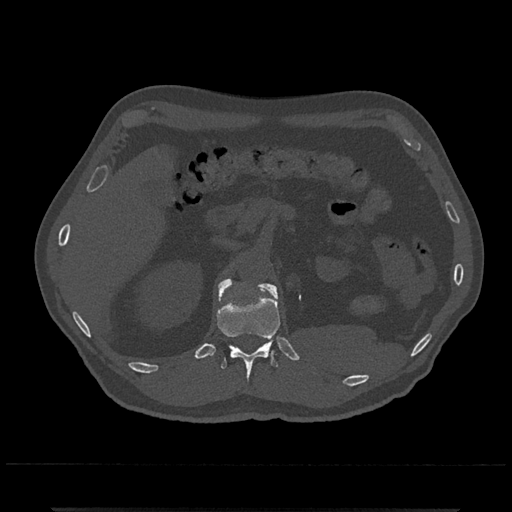
CT including the spine, one axial slice. Slice 418 of 797 in the series (ordered by position). Bone window (W 1800 / L 400 HU). 0.5 mm slice thickness. 512 × 512 image matrix, field of view 393 × 393 mm. Male patient, age 67 years. From the clinical record (not read from this slice): primary cancer: prostate.
Structures marked on this image (semi-automatic segmentation, software-assisted and operator-edited):
- L1 vertebra: bounding box (x1, y1, x2, y2) in pixels: (218, 280, 277, 297)
- T12 vertebra: (217, 279, 280, 381)